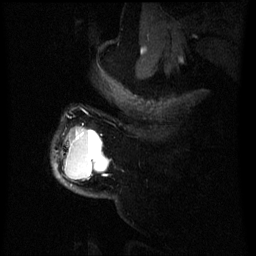
Breast MRI (dynamic contrast-enhanced), one sagittal slice; position 52 of 60 along the scan axis; dynamic contrast-enhanced series, image 2 of 3 at this slice position (ordered by acquisition); 1.5 T; TE 4.2 ms, TR 8 ms; 2.5 mm slice thickness; 256 × 256 image matrix, field of view 200 × 200 mm. Patient: female, 50 years.
Annotated regions visible in this slice (semi-automatically segmented with operator editing):
- analysis volume of interest (the breast-tissue region the enhancement analysis was run in; not a lesion): bounding box <54,128,109,181> (left, top, right, bottom; pixels)
- tumour enhancement mask (voxels above the 70 % enhancement threshold inside the analysis volume of interest): <104,174,106,177>